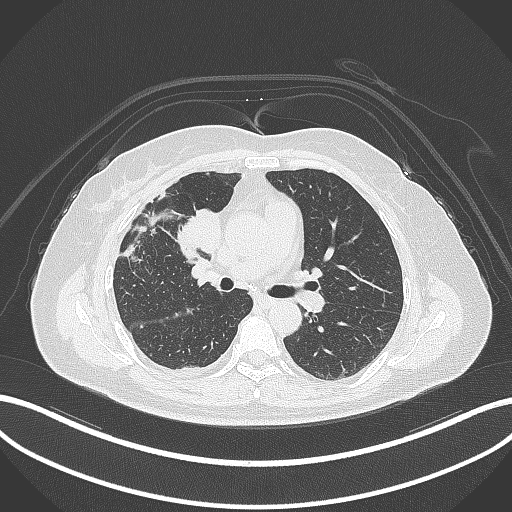
Chest CT, one axial slice. Slice 161 of 305 in the series (ordered by position). Reconstruction kernel B70f. Lung window (W 1500 / L -600 HU). 512 × 512 image matrix, field of view 400 × 400 mm. Patient: female, 52 years. From the clinical record (not read from this slice): clinical TNM (as recorded): T3 N1 M1.
Outlined on this slice (rectangle marked by the reading radiologist):
- lung tumour (recorded histology: adenocarcinoma): box from (x=173, y=207) to (x=223, y=261) px